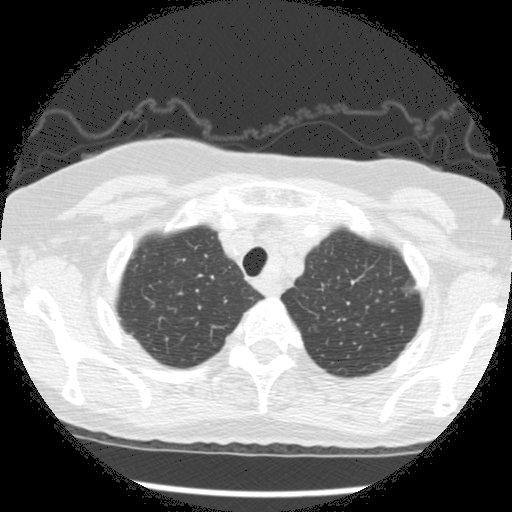
Axial slice from a low-dose chest CT screening exam, second screening round (one year after baseline), lung window (W 1500 / L -600 HU), standard (soft-tissue) reconstruction kernel (STANDARD), 120 kVp, slice 31 of 266 in the series, 512 × 512 image matrix. Female, age 73 years at enrolment.
- Expert reader's lesion annotation, bounding box [x1, y1, x2, y2] px = [381, 255, 430, 305].
- The screening reader recorded 3 non-calcified nodules or masses ≥4 mm on this exam; which of them this box marks is not recorded.